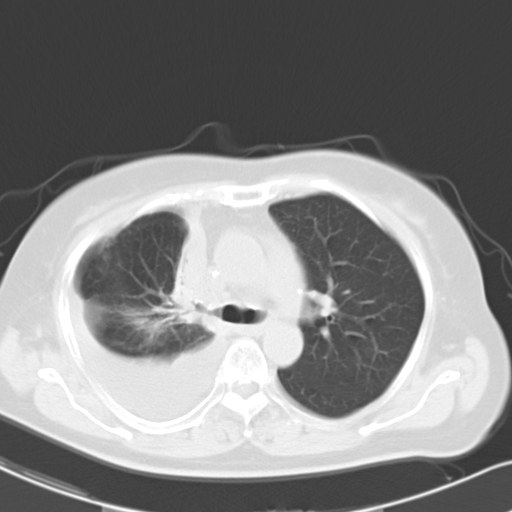
Chest CT, one axial slice. Slice 18 of 26 in the series (ordered by position). Reconstruction kernel B40f. Lung window (W 1500 / L -600 HU). 512 × 512 image matrix, field of view 328 × 328 mm. Patient: female, 69 years. Case-level facts recorded for this patient, not image findings: clinical TNM (as recorded): T2a N0 M1c.
Outlined on this slice (bounding box drawn by a radiologist):
- lung tumour (recorded histology: adenocarcinoma): bounding box (x1, y1, x2, y2) in pixels: (175, 209, 223, 339)